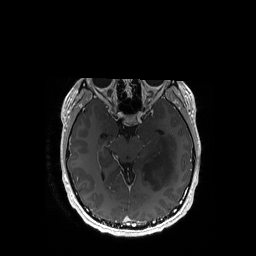
Brain MRI from a brain-tumour surgery series, one axial slice; slice 104 of 192 in the series (ordered by position); T1-weighted post-contrast; 1 mm slice thickness; 256 × 256 image matrix, field of view 256 × 256 mm. From the clinical record (not read from this slice): histopathology: Astrocytoma; WHO grade: 3; IDH mutation: yes.
Annotated regions visible in this slice (outlined manually by an expert reader):
- tumour: bounding box (x1, y1, x2, y2) in pixels: (143, 132, 177, 191)